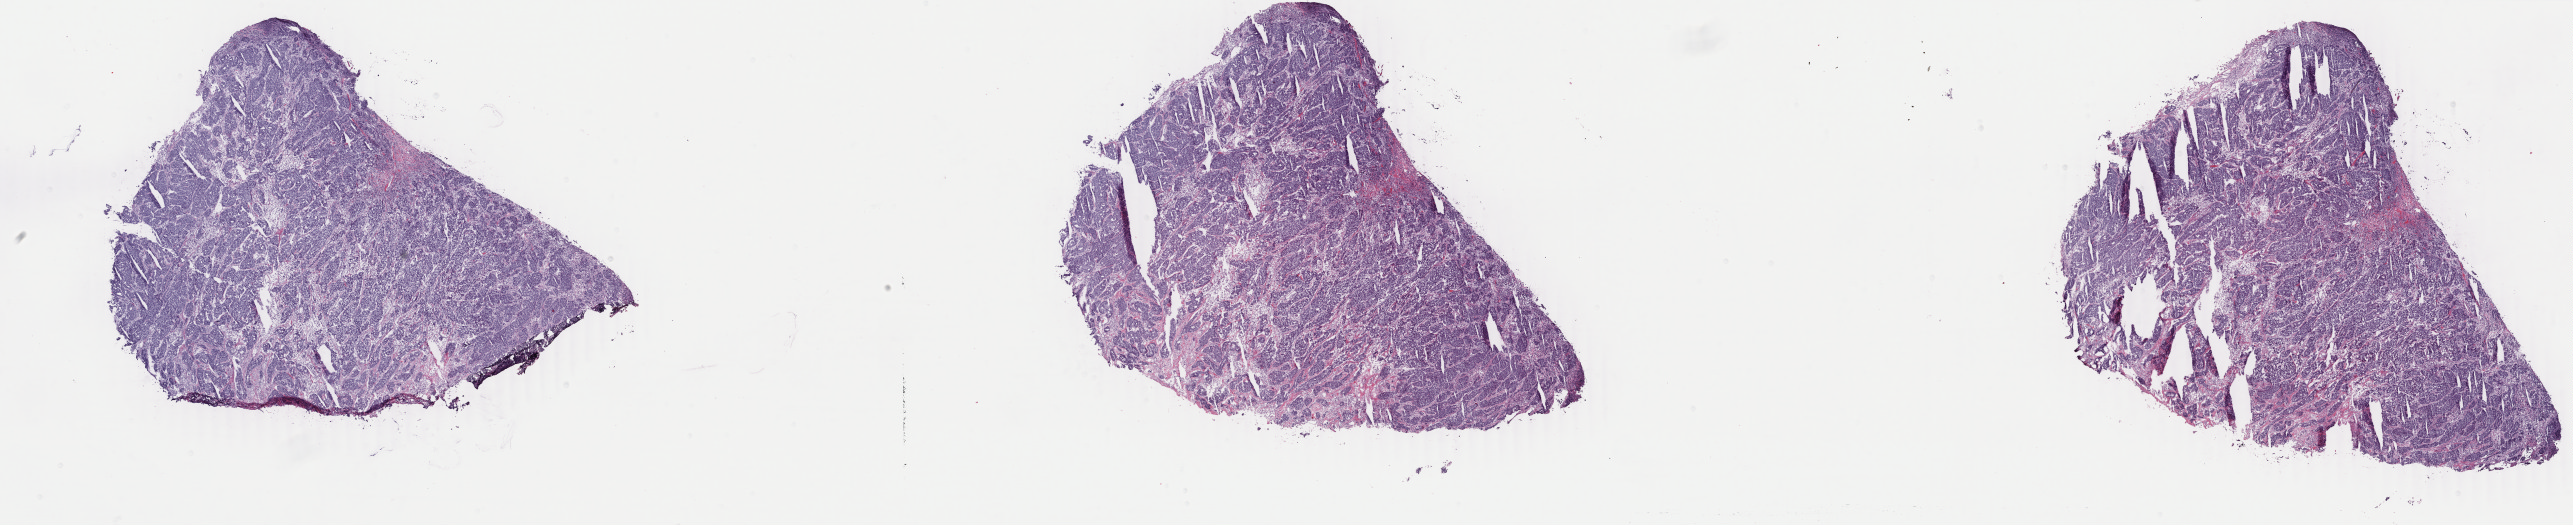
Digitized H&E tissue section (whole slide) — low-resolution overview of the scanned area, about 40.9 x 8.4 mm (slide scanned at 40x). Frozen section from the top of the tissue portion. Sample: primary tumour, breast. Patient: female, age at initial diagnosis 56 years. Slide review estimates, as recorded: tumour cells 88%, tumour nuclei 90%, normal cells 0%, stromal cells 10%, necrosis 2%. Infiltration values recorded for this section: lymphocyte infiltration 1%, monocyte infiltration 0%, neutrophil infiltration 0%.
Pathologic diagnosis: Infiltrating duct carcinoma, NOS. TNM: T2 N0 M0. AJCC pathologic stage: IIA.